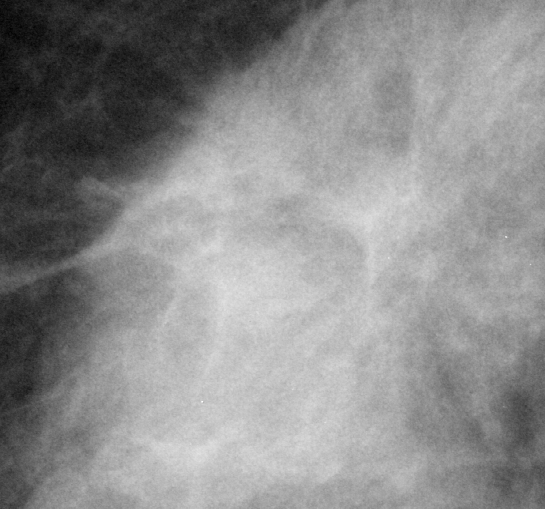
Crop from a digitized film mammogram around one marked abnormality, right breast, MLO view.
- Mass, shape irregular, margins spiculated; BI-RADS assessment category 5; pathology result (as recorded, not read from the image): malignant.